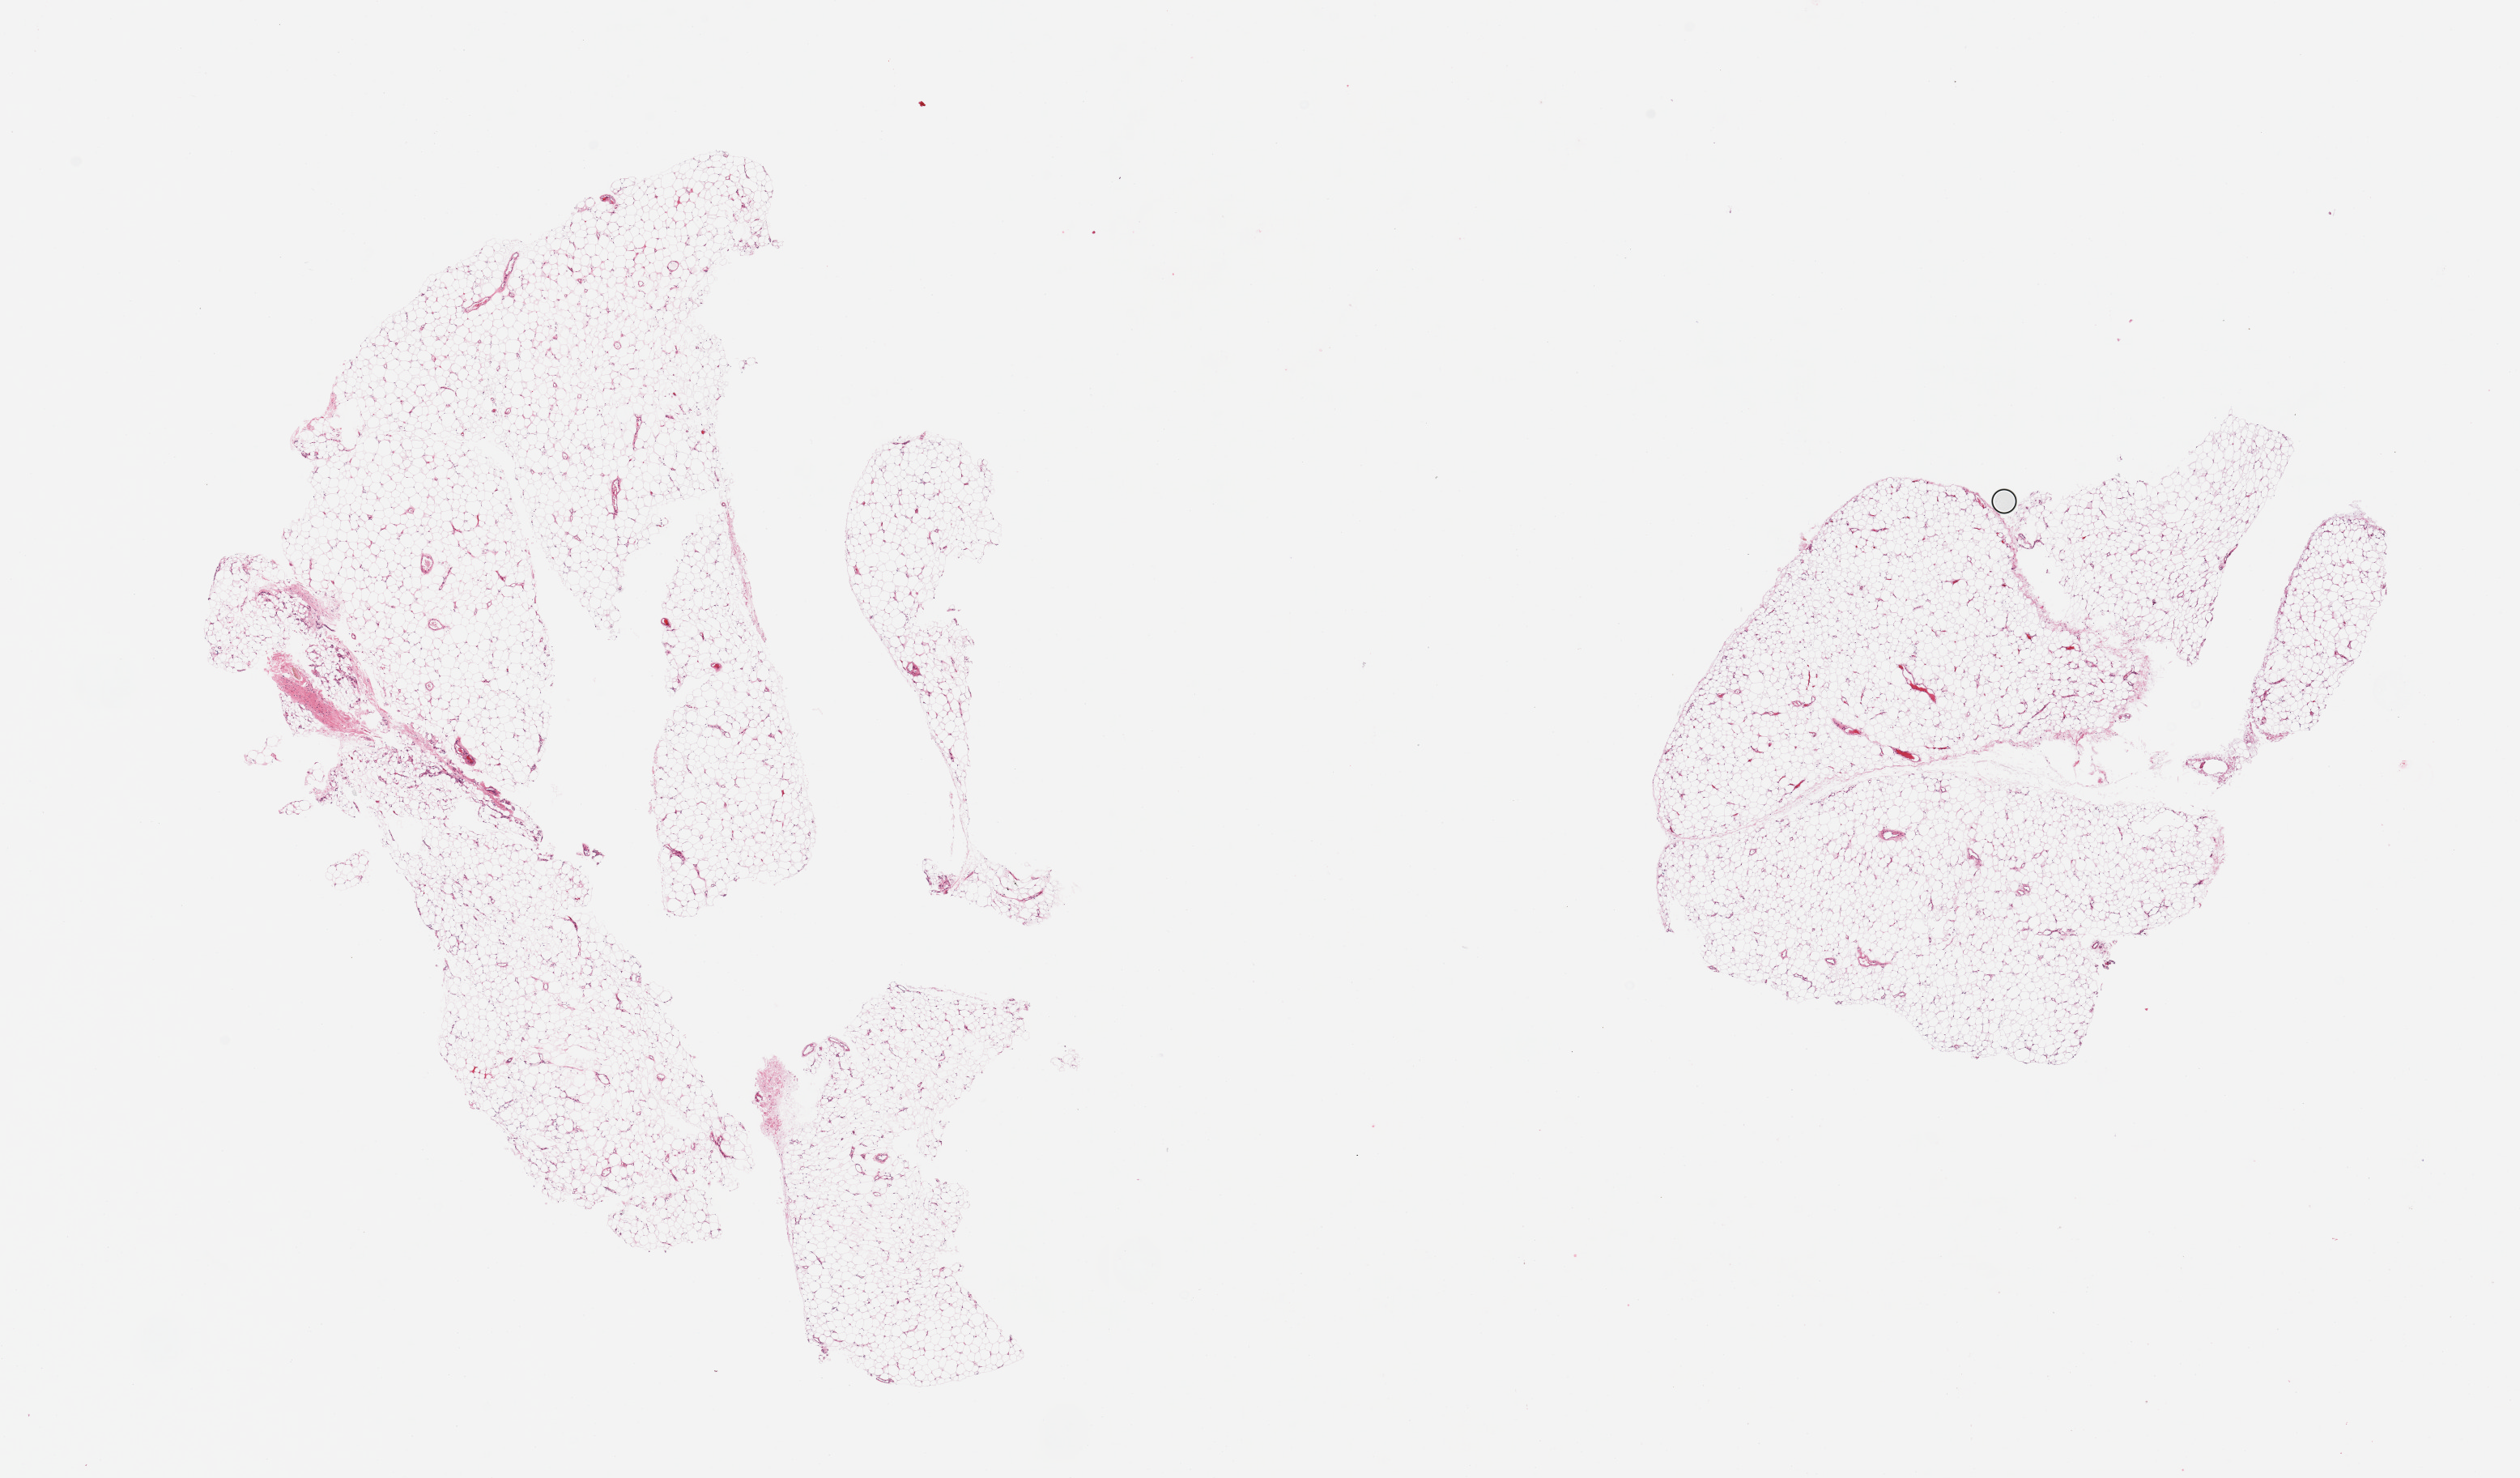
Whole-slide image, H&E stain, brightfield, shown as a low-resolution overview of the whole scanned area (about 24.6 x 14.4 mm). PAXgene-fixed, paraffin-embedded tissue. Target tissue: adipose tissue. Tissue donor sample. Donor sex: male.
Reviewer comment on this tissue sample: 2 pieces, trace fascia/vascular elements.